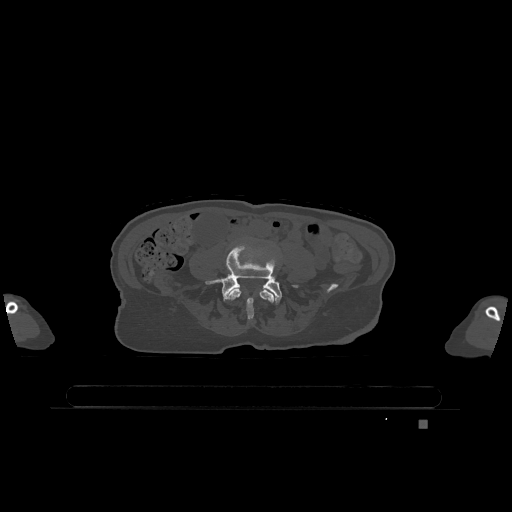
CT including the spine, one axial slice; slice 263 of 1317 in the series (ordered by position); bone window (W 1800 / L 400 HU); 0.5 mm slice thickness; 512 × 512 image matrix, field of view 500 × 500 mm. Female patient, age 74 years. From the clinical record (not read from this slice): primary cancer: lung; vertebrae with lytic lesions (as recorded): T1, T4, T5, T6, L4, L5.
Outlined on this slice (semi-automatic segmentation, software-assisted and operator-edited):
- L4 vertebra: bounding box [x1, y1, x2, y2] px = [227, 289, 274, 320]
- L5 vertebra: [206, 246, 297, 305]